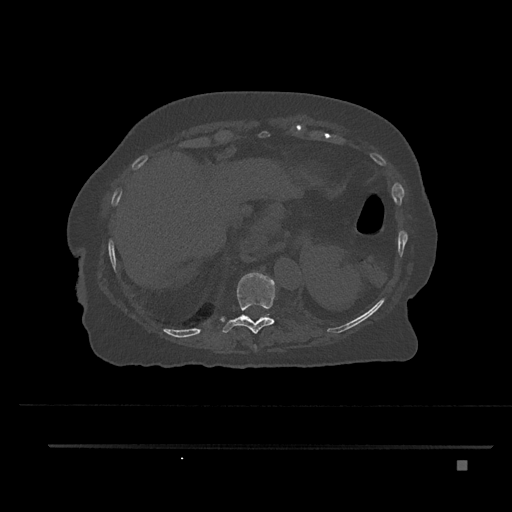
CT including the spine, one axial slice; position 352 of 797 along the scan axis; 120 kVp; bone window (W 1800 / L 400 HU); 0.5 mm slice thickness; 512 × 512 image matrix, field of view 437 × 437 mm. Female patient, age 76 years. From the clinical record (not read from this slice): primary cancer: lung; vertebrae with lytic lesions (as recorded): T11, L3.
Outlined on this slice (semi-automatically segmented with operator editing):
- T10 vertebra: box from (x=220, y=272) to (x=275, y=334) px
- T9 vertebra: (x=254, y=345)–(x=257, y=351)